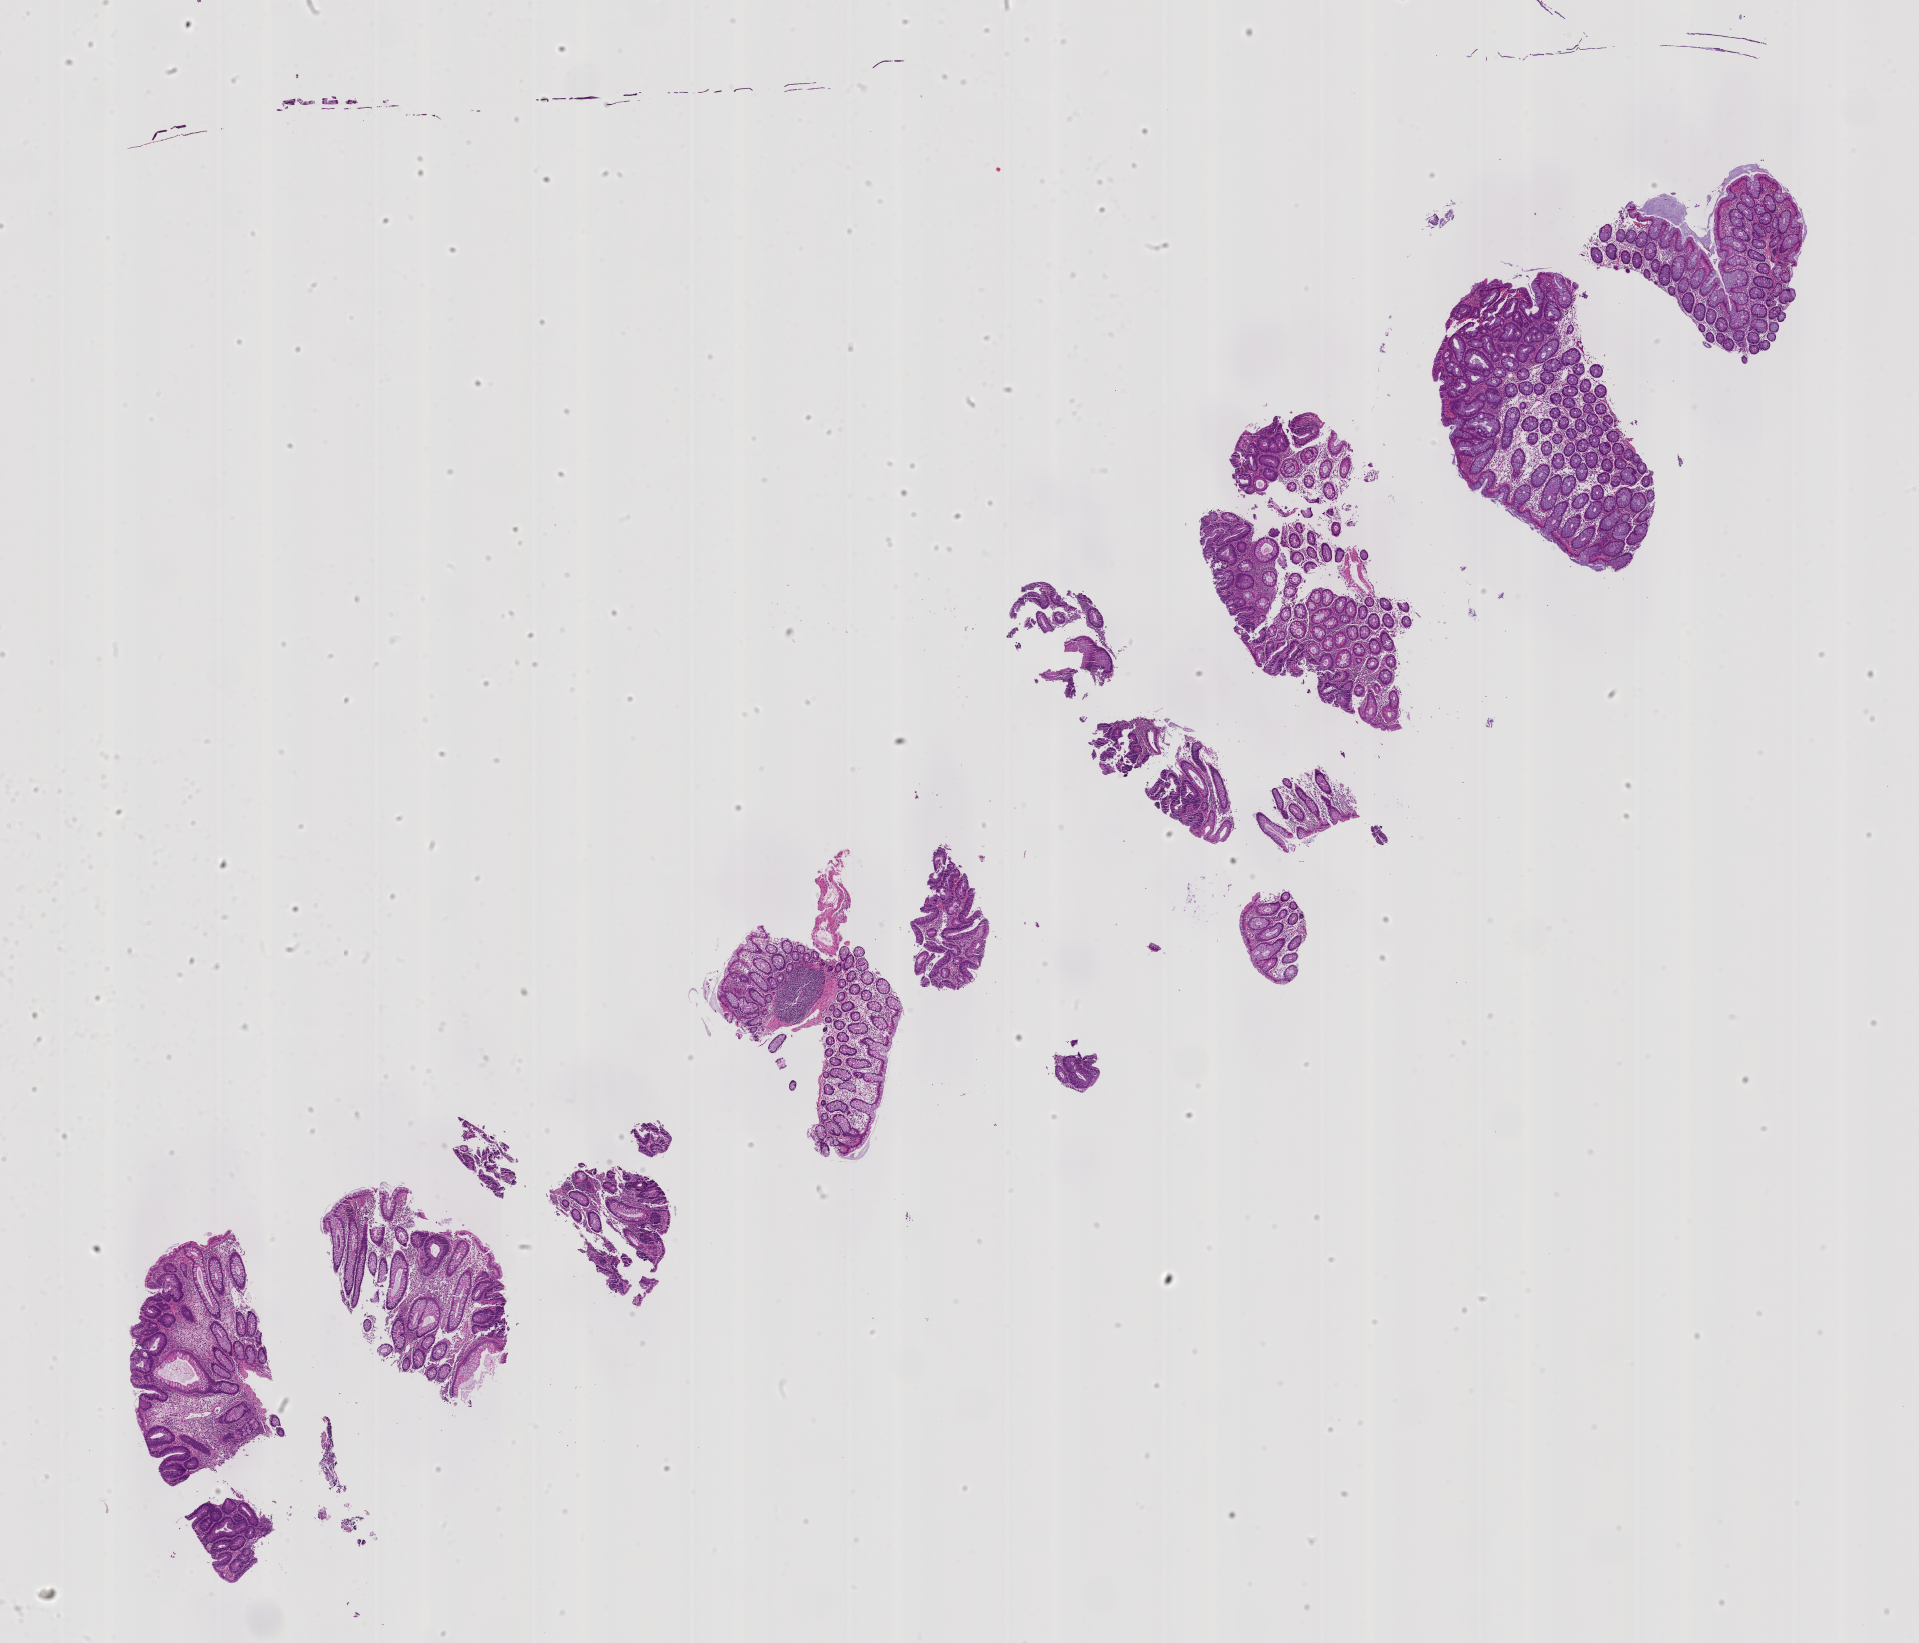
Haematoxylin and eosin whole-slide image of a colon biopsy — whole scanned area (about 15.4 x 13.1 mm) shown as a low-resolution overview; formalin-fixed, paraffin-embedded (FFPE) tissue; ascending colon. Patient sex: female.
Lesion category (as recorded): premalignant.